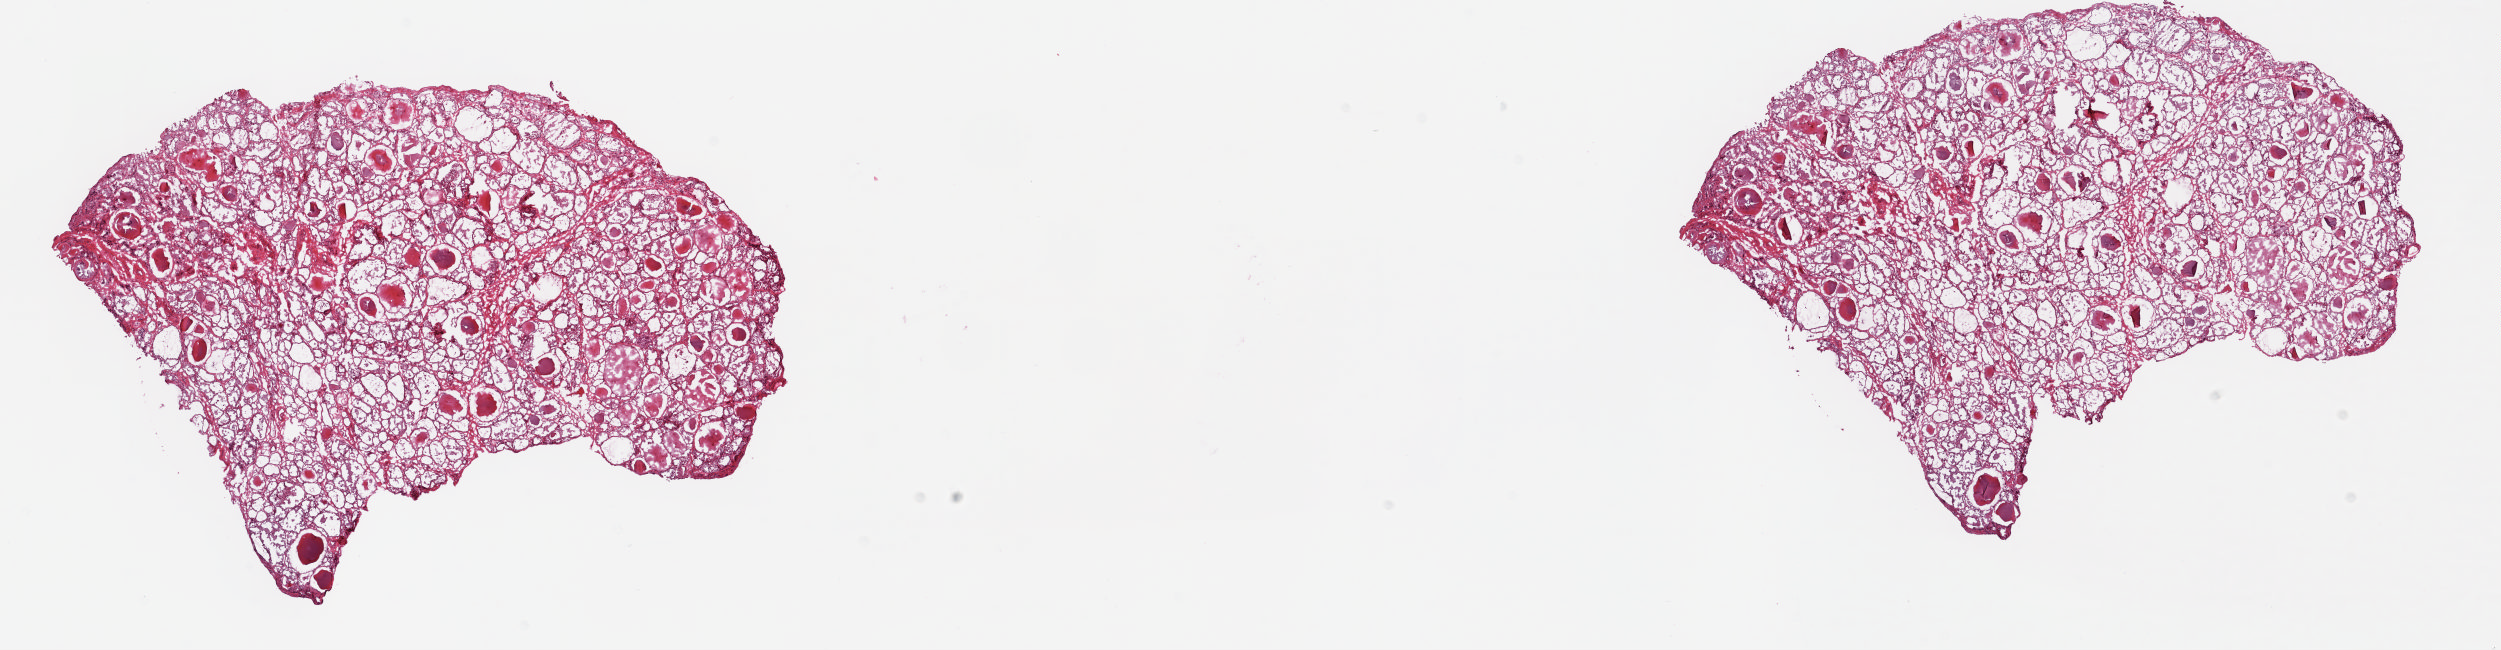
Hematoxylin and eosin (H&E) stained whole-slide image, shown as a low-resolution overview of the whole scanned area (about 19.8 x 5.2 mm, acquisition: 20x scan); frozen section from the top of the tissue portion; thyroid, solid tissue normal (non-tumour tissue) sample. Male patient; age at initial diagnosis 76 years. Composition of this section per pathologist review: tumour cells 0%, tumour nuclei 0%, normal cells 100%, stromal cells 0%, necrosis 0%. Infiltration values recorded for this section: lymphocyte infiltration 0%, monocyte infiltration 0%, neutrophil infiltration 0%.
This section: solid tissue normal sample (biorepository sample class). Patient diagnosis: Papillary adenocarcinoma, NOS (thyroid gland).